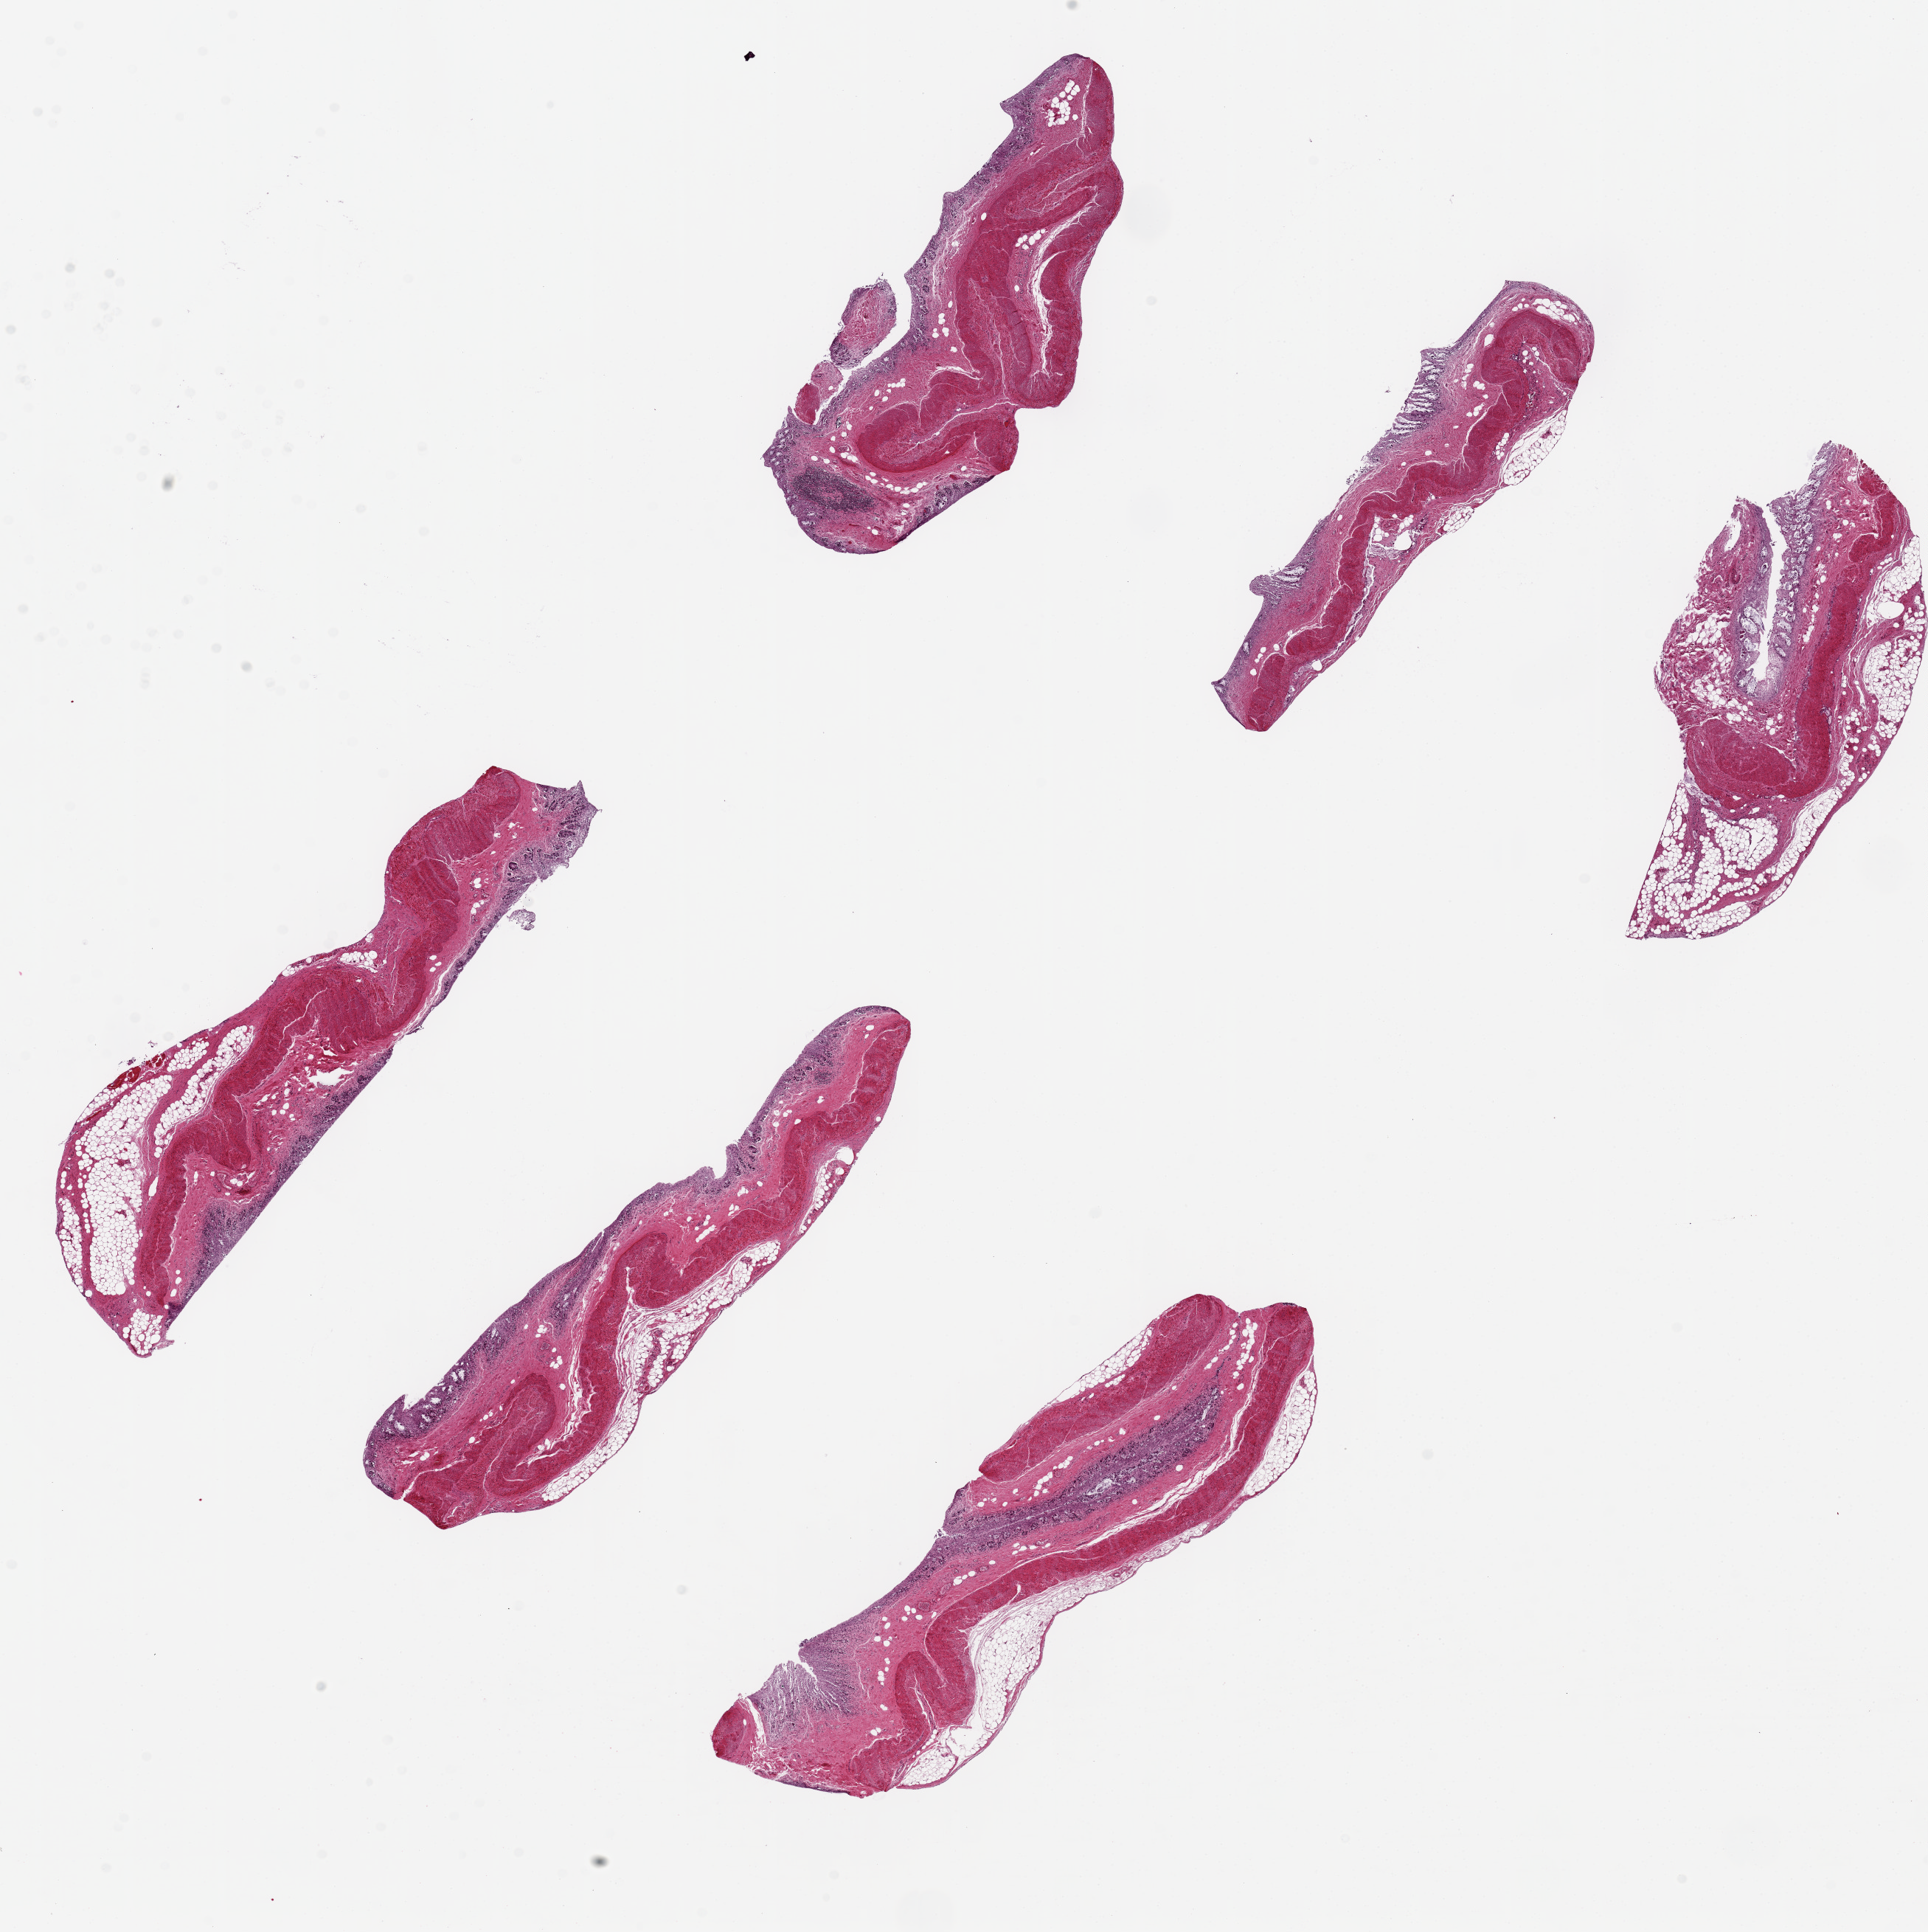
Whole-slide image, haematoxylin and eosin stain — low-resolution overview of the scanned area, about 20.7 x 20.7 mm (from a 20x scan), PAXgene-fixed paraffin-embedded (PFPE) section, sampled site (target tissue): transverse colon, donor tissue sample. Male donor.
Review note (as recorded): 6 ~6x2.5mm pieces. Mucosa is ~10-20% of thickness but epithelial component nearly totally autolyzed.